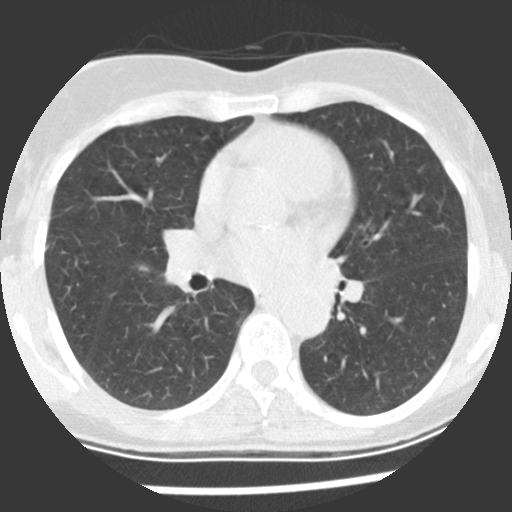
Low-dose screening chest CT, one axial slice; slice 115 of 225 in the series (ordered by position); reconstruction kernel STANDARD; 120 kVp; lung window (W 1500 / L -600 HU); 2.5 mm slice thickness; 512 × 512 image matrix, field of view 270 × 270 mm.
Annotated regions visible in this slice (outlined manually by an expert reader):
- lesion 1 (tumor, upper lobe of right lung): bounding box <140,266,148,271> (left, top, right, bottom; pixels)